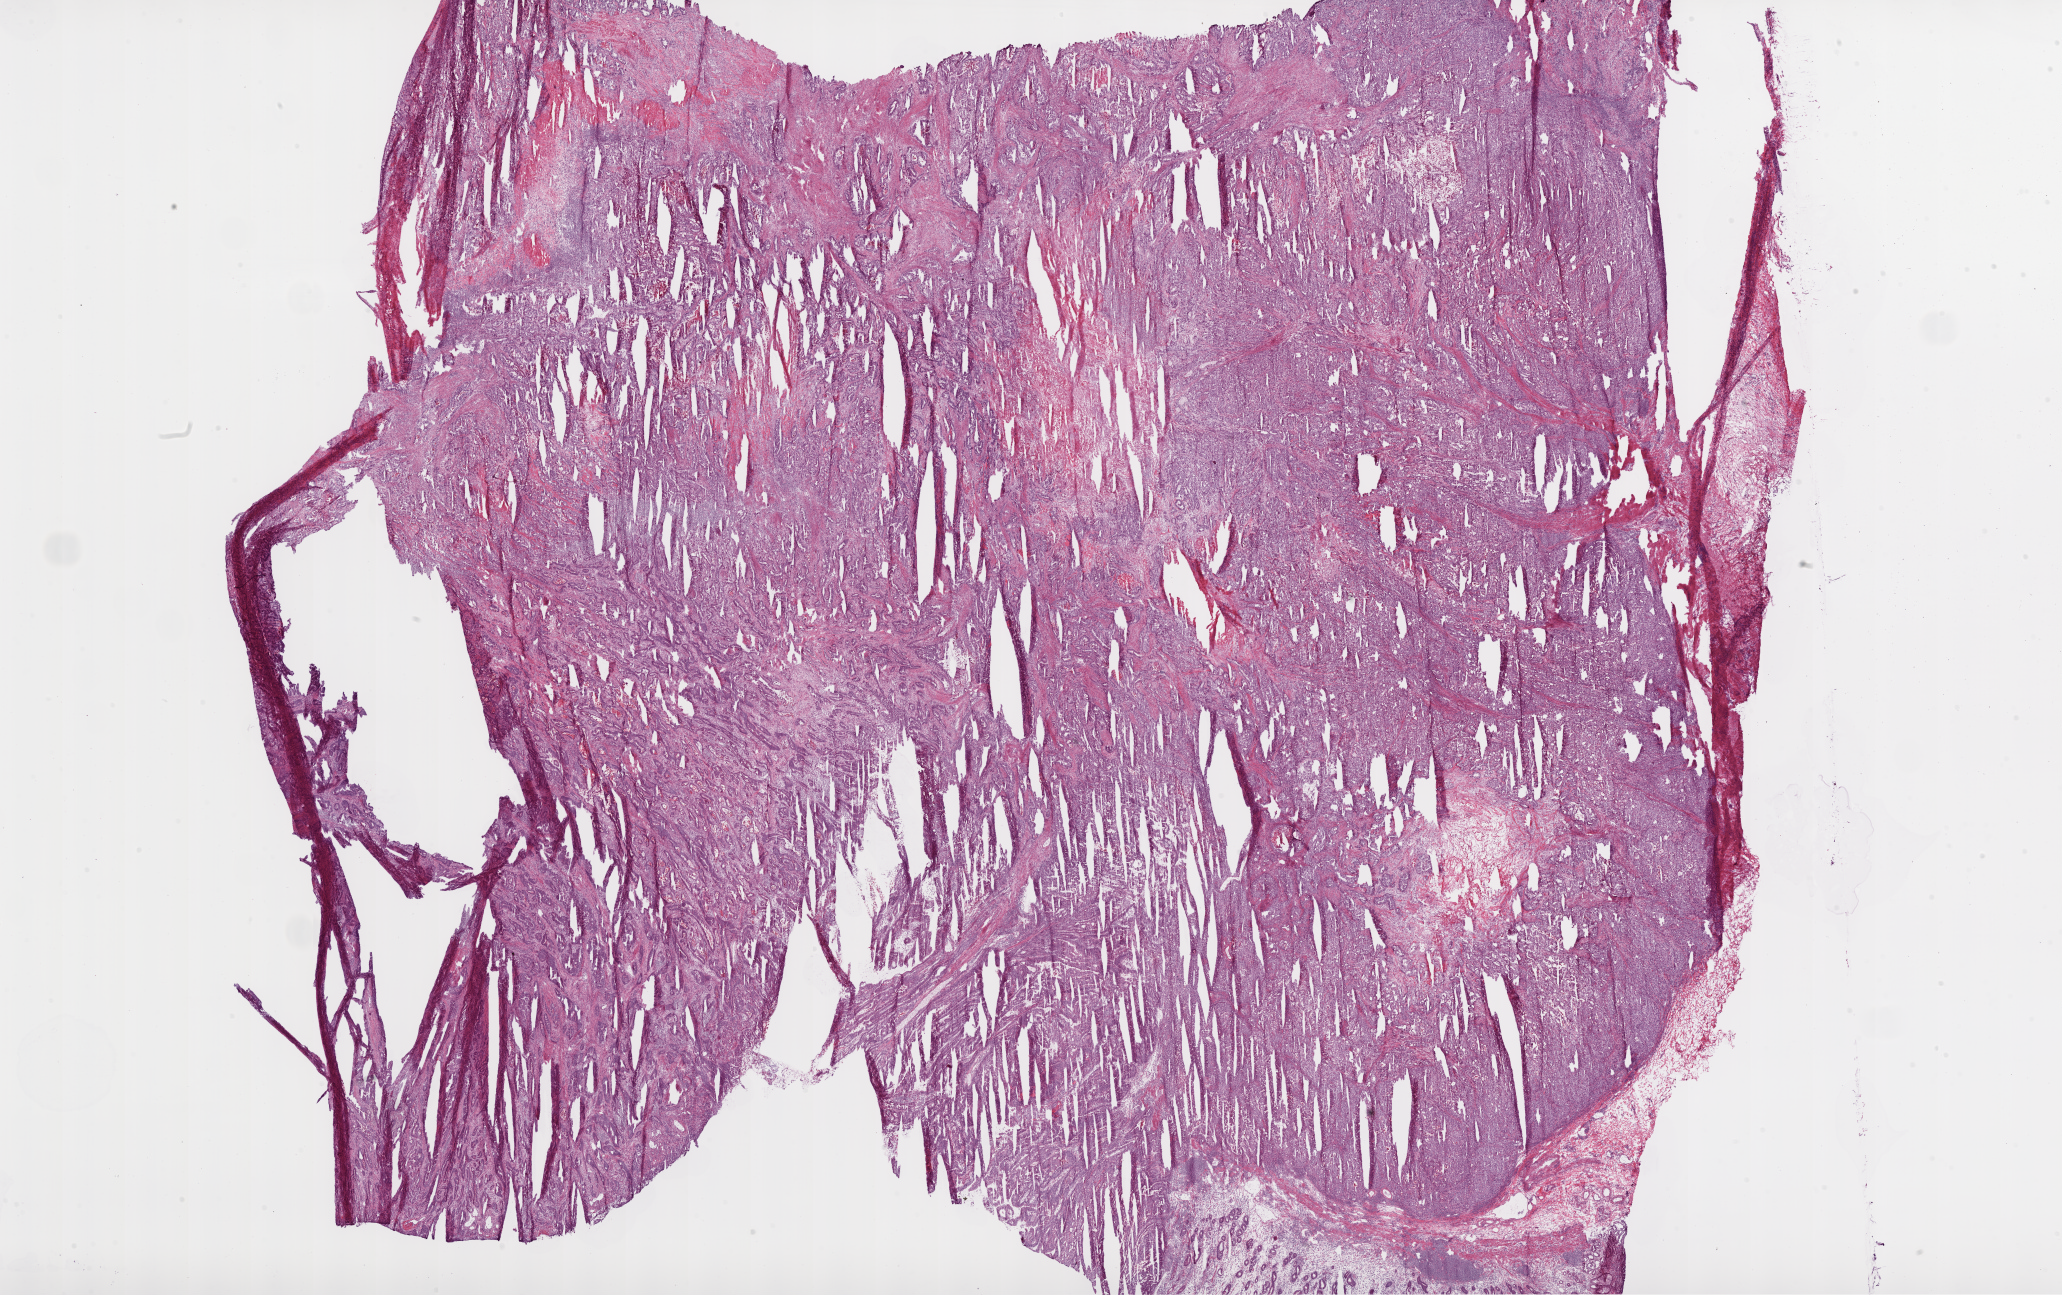
Digitized H&E tissue section (whole slide) — shown as a low-resolution overview of the whole scanned area (about 33.1 x 20.8 mm, slide scanned at 20x), frozen section from the bottom of the tissue portion, sample: primary tumour, stomach. Patient: male, age at initial diagnosis 70 years. Histologic grade: G2 (moderately differentiated). Composition of this section per pathologist review: tumour cells 84%, tumour nuclei 85%, normal cells 5%, stromal cells 8%, necrosis 3%.
* pathologic diagnosis: Adenocarcinoma, NOS (gastric antrum)
* lymph nodes positive (case pathology): 1 of 8 examined
* AJCC pathologic stage: IIIA (6th edition)